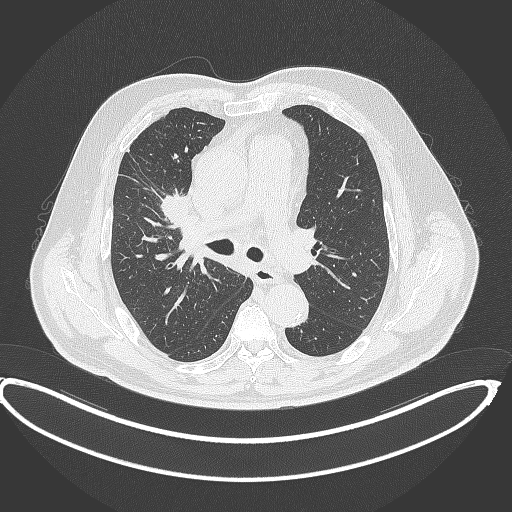
Chest CT, one axial slice; slice 257 of 390 in the series (ordered by position); 120 kVp; lung window (W 1500 / L -600 HU); 1 mm slice thickness; 512 × 512 image matrix, field of view 448 × 448 mm. Male patient, age 62 years. Case-level facts recorded for this patient, not image findings: clinical TNM (as recorded): T1c N3 M1c.
Outlined on this slice (bounding box drawn by a radiologist):
- lung tumour (recorded histology: adenocarcinoma): box from (x=156, y=193) to (x=191, y=222) px